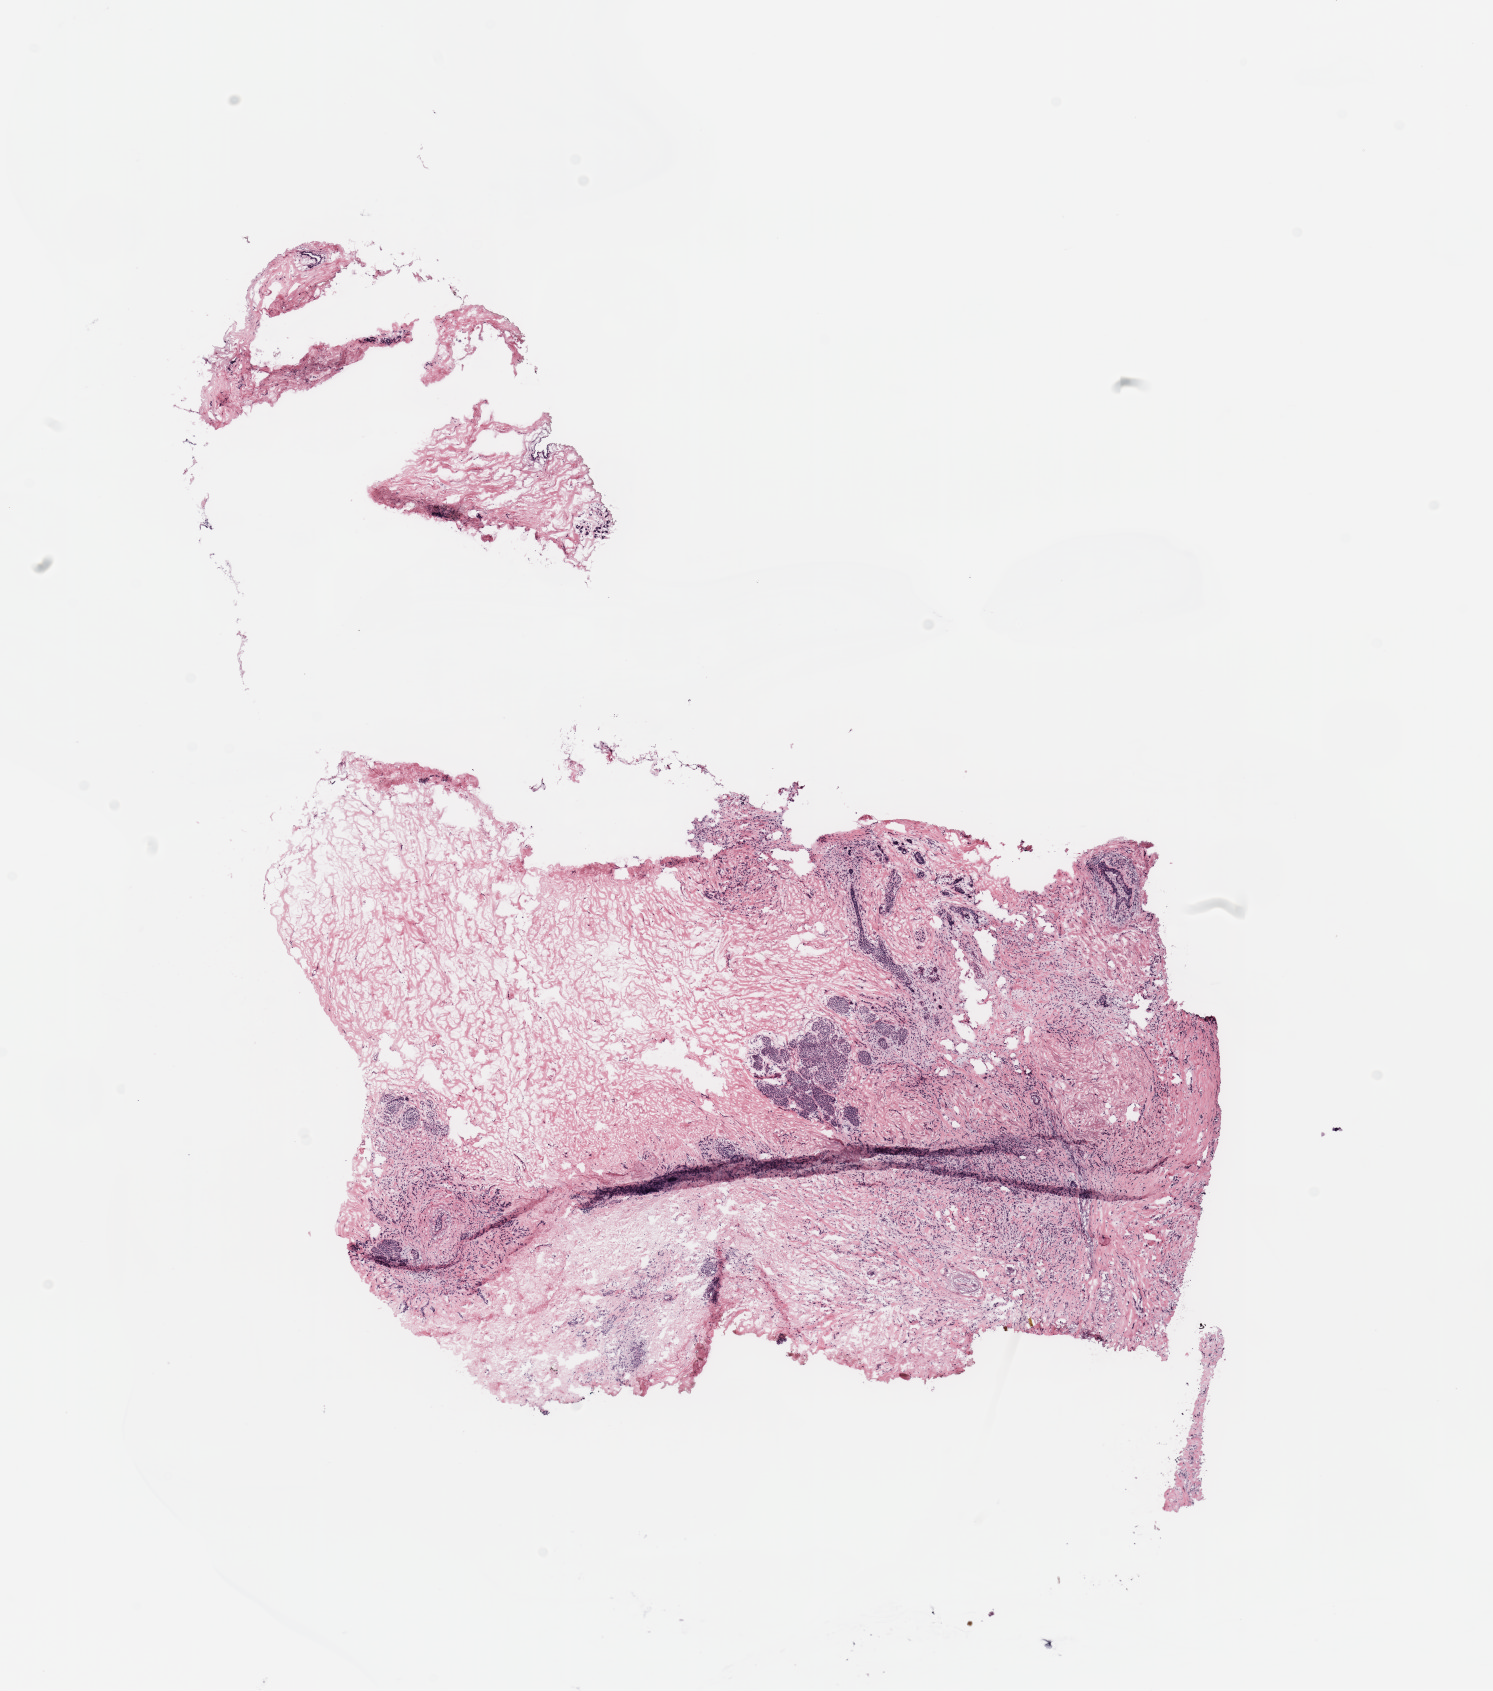
Digitized Hematoxylin and eosin (H&E) stained tissue section (whole slide), whole scanned area (about 11.8 x 13.4 mm) shown as a low-resolution overview; tumour tissue sample, breast. Female, 66 y/o.
Histologic diagnosis: Infiltrating lobular carcinoma, NOS. AJCC pathologic stage: IIIA.